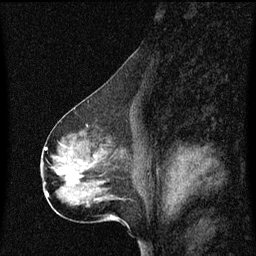
Breast MRI (dynamic contrast-enhanced), one sagittal slice; slice 31 of 60 in the series (ordered by position); dynamic contrast-enhanced series, image 2 of 3 at this slice position (ordered by acquisition); 1.5 T; TE 4.2 ms, TR 8.4 ms; 2 mm slice thickness; 256 × 256 image matrix, field of view 200 × 200 mm. Female patient, age 50 years. From the clinical record (not read from this slice): setting: breast cancer imaged before/during neoadjuvant chemotherapy; receptor status: HR-positive, HER2-negative.
Structures marked on this image (semi-automatically segmented with operator editing):
- analysis volume of interest (the breast-tissue region the enhancement analysis was run in; not a lesion): bounding box <55,140,124,191> (left, top, right, bottom; pixels)
- tumour enhancement mask (voxels above the 70 % enhancement threshold inside the analysis volume of interest): <71,172,78,179>